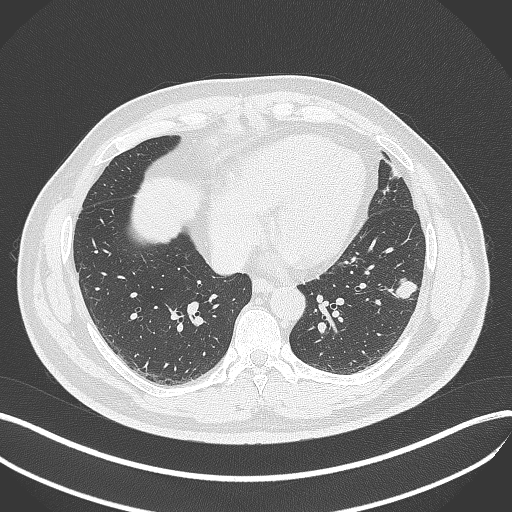
Chest CT, one axial slice. Slice 151 of 429 in the series (ordered by position). Reconstruction kernel B70f. 120 kVp. Lung window (W 1500 / L -600 HU). 1 mm slice thickness. 512 × 512 image matrix, field of view 400 × 400 mm. Male patient, age 39 years. From the clinical record (not read from this slice): clinical TNM (as recorded): T2a N0 M0; histopathological grade: G2-3.
Structures marked on this image (bounding box drawn by a radiologist):
- lung tumour (recorded histology: adenocarcinoma): box from (x=387, y=278) to (x=419, y=302) px